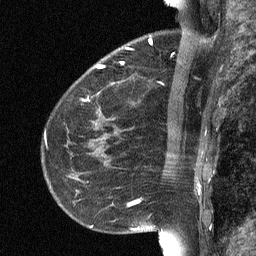
Breast MRI (dynamic contrast-enhanced), one sagittal slice; position 22 of 64 along the scan axis; dynamic contrast-enhanced study with each time point stored as its own series, time point 2 of 3 at this slice position (early post-contrast, ordered by acquisition time); 1.5 T; TE 4.8 ms, TR 27 ms; 256 × 256 image matrix, field of view 180 × 180 mm. Patient: female, 51 years. Case-level facts recorded for this patient, not image findings: setting: breast cancer imaged before/during neoadjuvant chemotherapy; receptor status: HR-positive, HER2-negative.
Outlined on this slice (semi-automatic segmentation, software-assisted and operator-edited):
- analysis volume of interest (the breast-tissue region the enhancement analysis was run in; not a lesion): bounding box <72,34,182,118> (left, top, right, bottom; pixels)
- tumour enhancement mask (voxels above the 90 % enhancement threshold inside the analysis volume of interest): <97,41,152,68>